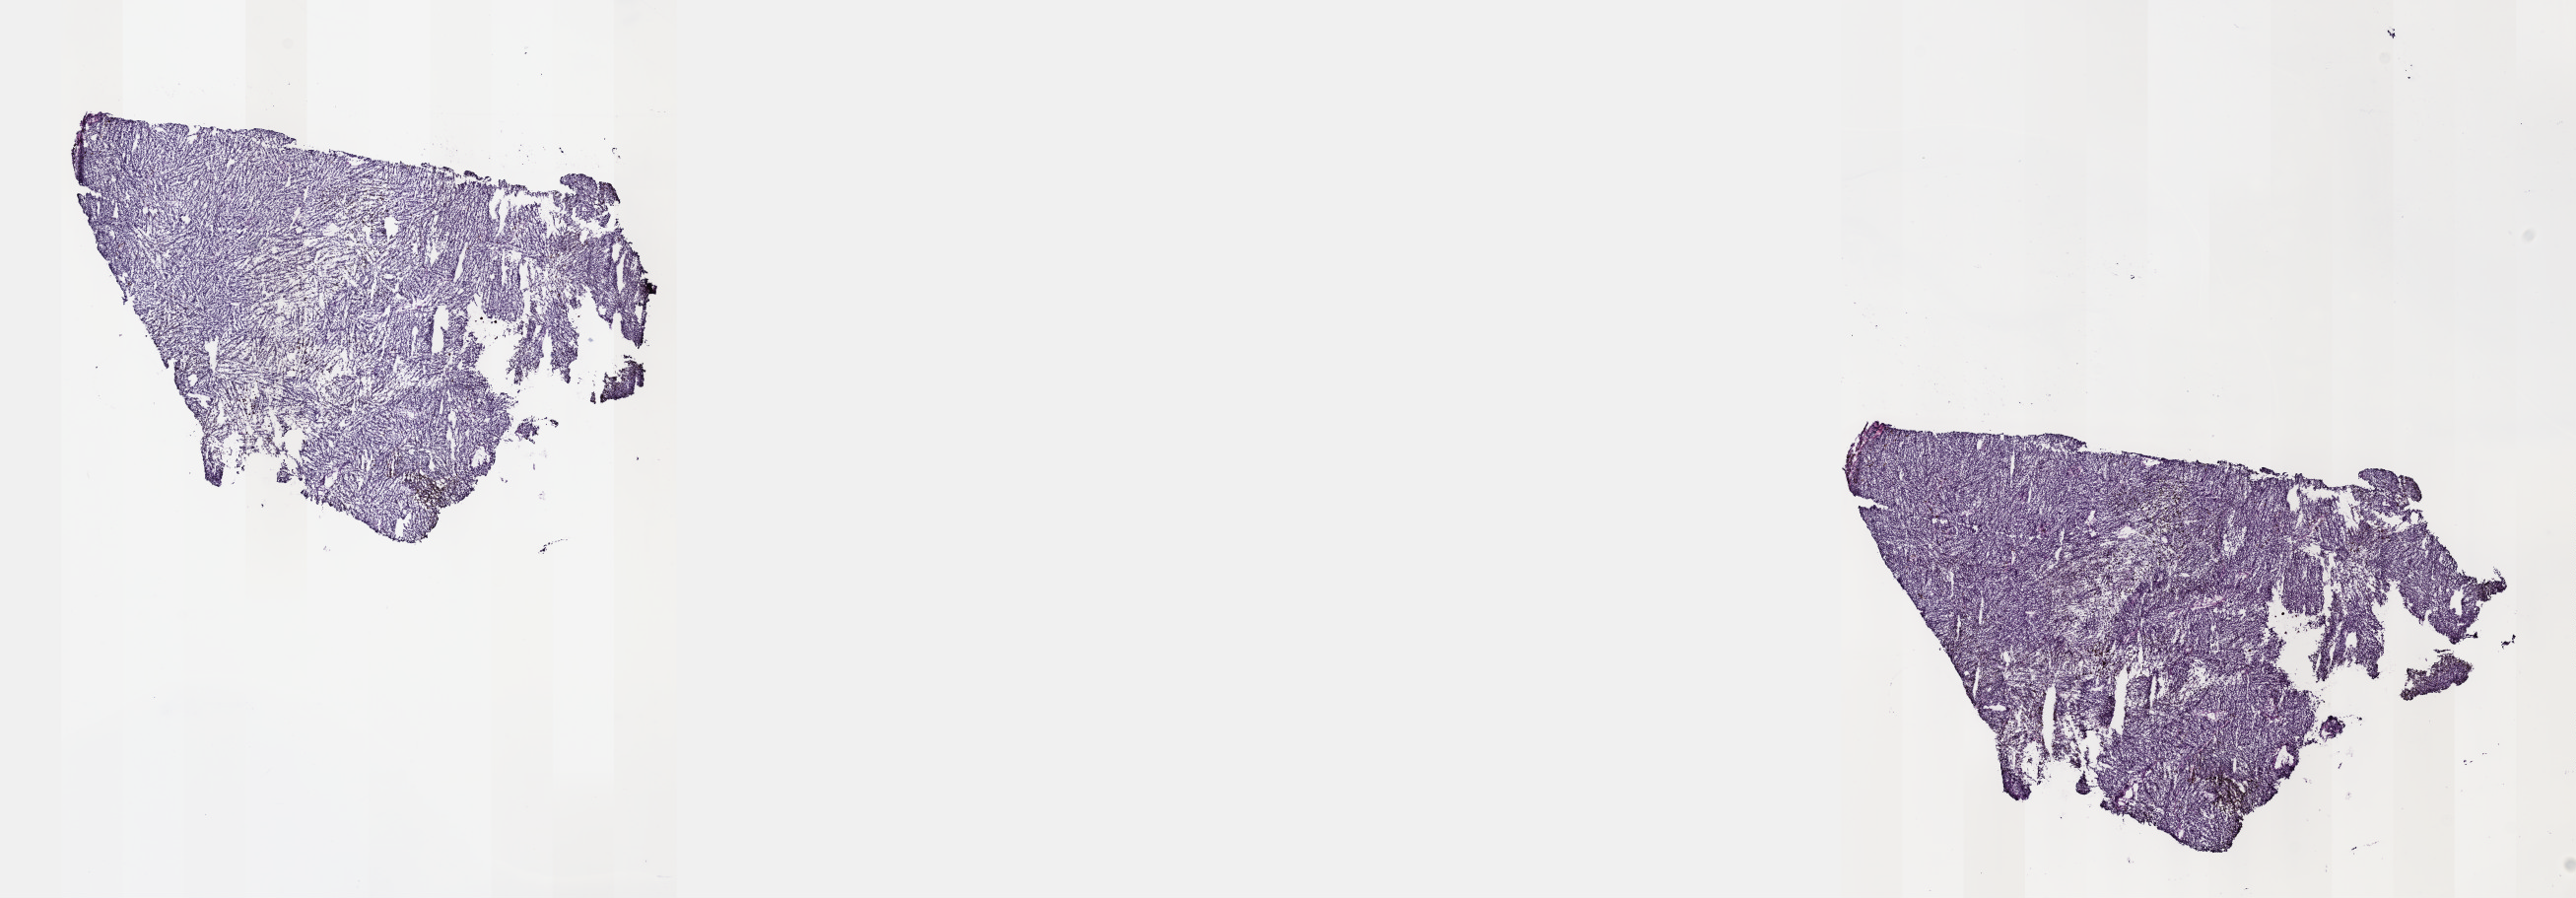
Digitized H&E tissue section (whole slide) — whole scanned area (about 21.1 x 7.4 mm) shown as a low-resolution overview, frozen section, primary tumour sample from the uvea. Male patient; age at initial diagnosis 57 years. Composition of this section per pathologist review: tumour cells 100%, tumour nuclei 80%, normal cells 0%, stromal cells 0%, necrosis 0%. Inflammatory infiltration, as recorded: lymphocyte infiltration 1%, monocyte infiltration 0%, neutrophil infiltration 0%.
Histologic diagnosis: Mixed epithelioid and spindle cell melanoma (choroid). AJCC pathologic stage: IIIB (7th edition). TNM: T4b N0 M0.